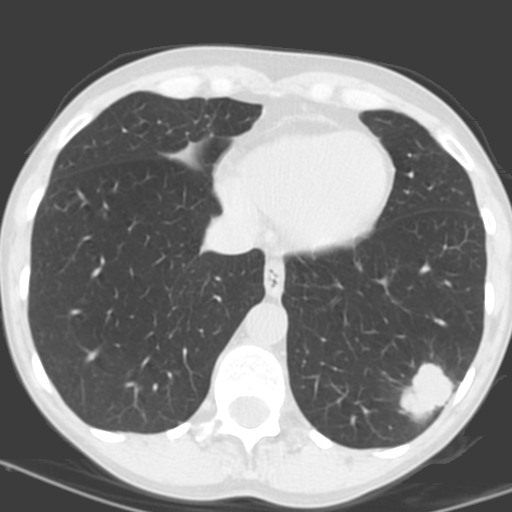
Axial slice from a low-dose chest CT screening exam; baseline screening round; lung window (W 1500 / L -600 HU); 3.2 mm slice thickness; standard (soft-tissue) reconstruction kernel (C); 512 × 512 image matrix, field of view 262 × 262 mm. Female participant, aged 56 years at enrolment.
- Expert-annotated lung lesion, bounding box [x1, y1, x2, y2] px = [390, 357, 466, 426].
- The exam's reader record, not a measurement of the box and not confirmed to be the same lesion: non-calcified nodule or mass ≥4 mm, left lower lobe, 31 × 23 mm, poorly defined margins, soft tissue attenuation, pre-existing on the prior screen: no.
- Official screen result: positive, change unspecified: nodule(s) >= 4 mm or enlarging nodule(s), mass(es), or other non-specific abnormalities suspicious for lung cancer.
- Later outcome: lung cancer diagnosed 27 days after this screen — squamous cell carcinoma, NOS, left lower lobe, poorly differentiated (G3), stage IB (AJCC 6th edition), 35 mm at pathology.